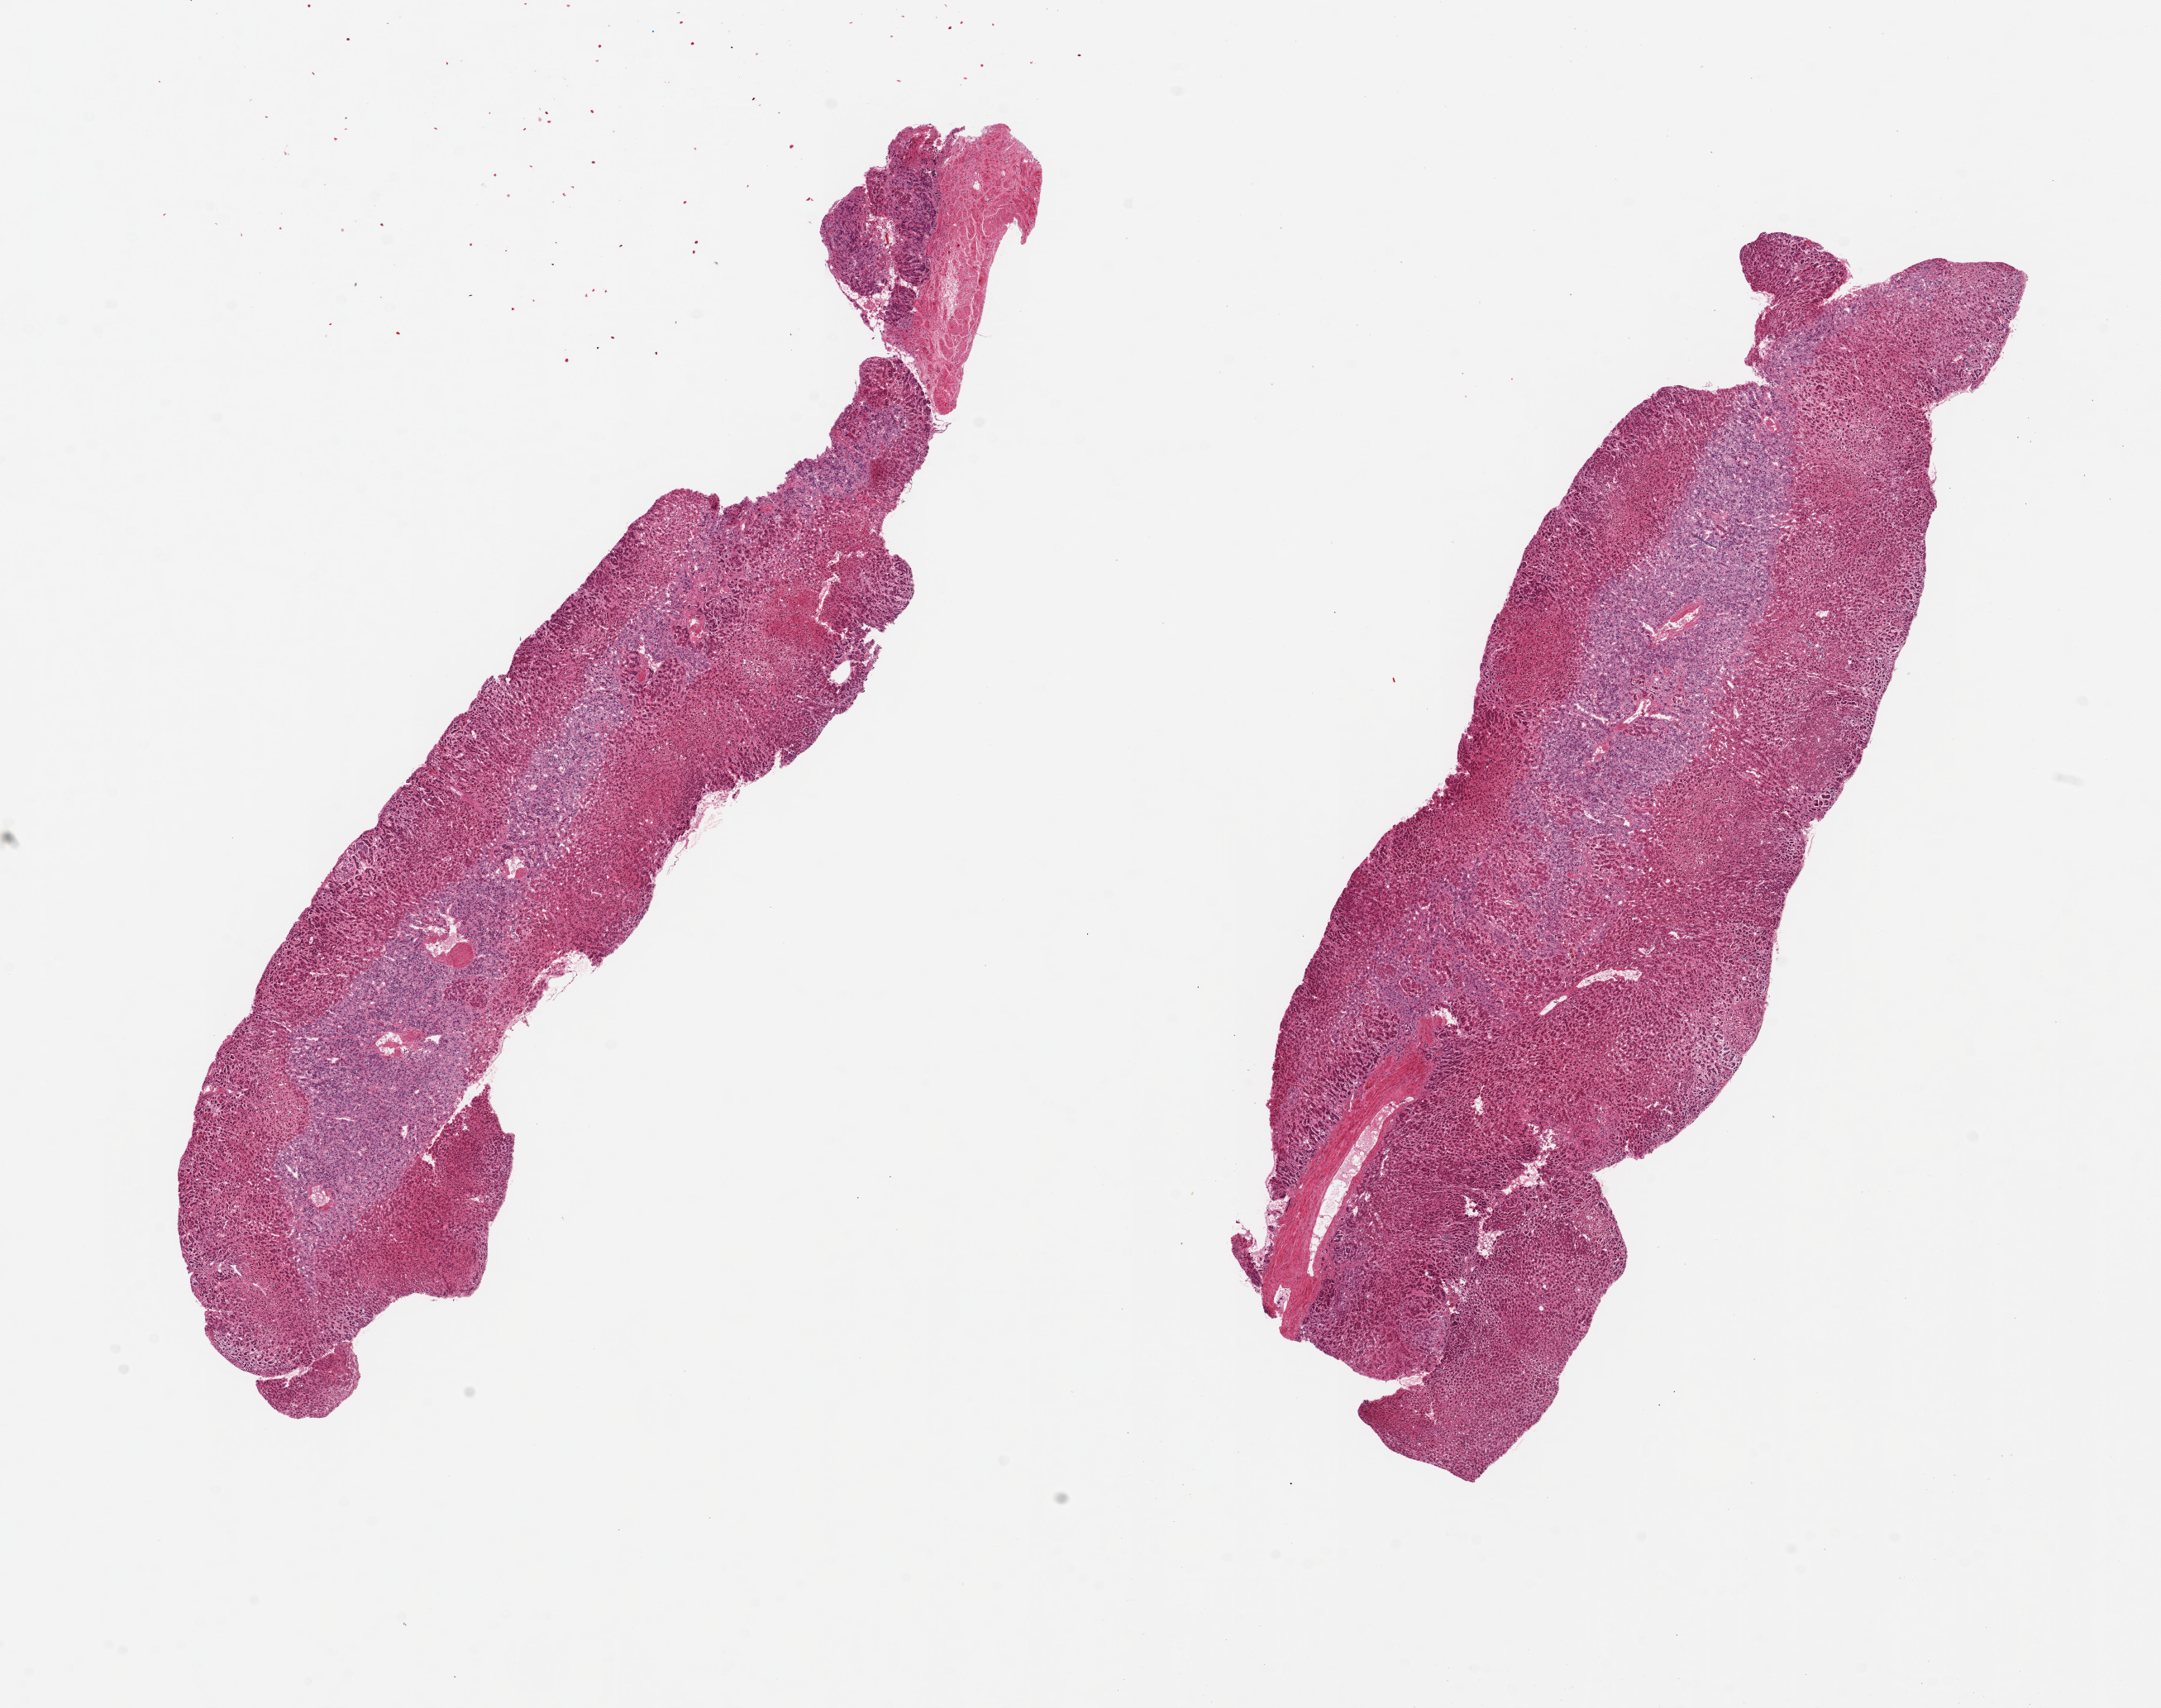
Digitized hematoxylin and eosin (H&E)-stained section — a low-resolution overview of the entire scanned area, about 20.7 x 16.3 mm (slide scanned at 20x); PAXgene-fixed paraffin-embedded (PFPE) section; sampled site (target tissue): adrenal gland; donor tissue sample. Donor sex: male.
Pathologist's review note for this sample: 2 pieces, 14x3 & 13x4mm; cortex and medulla well represented; no extraneous adipose tissue.